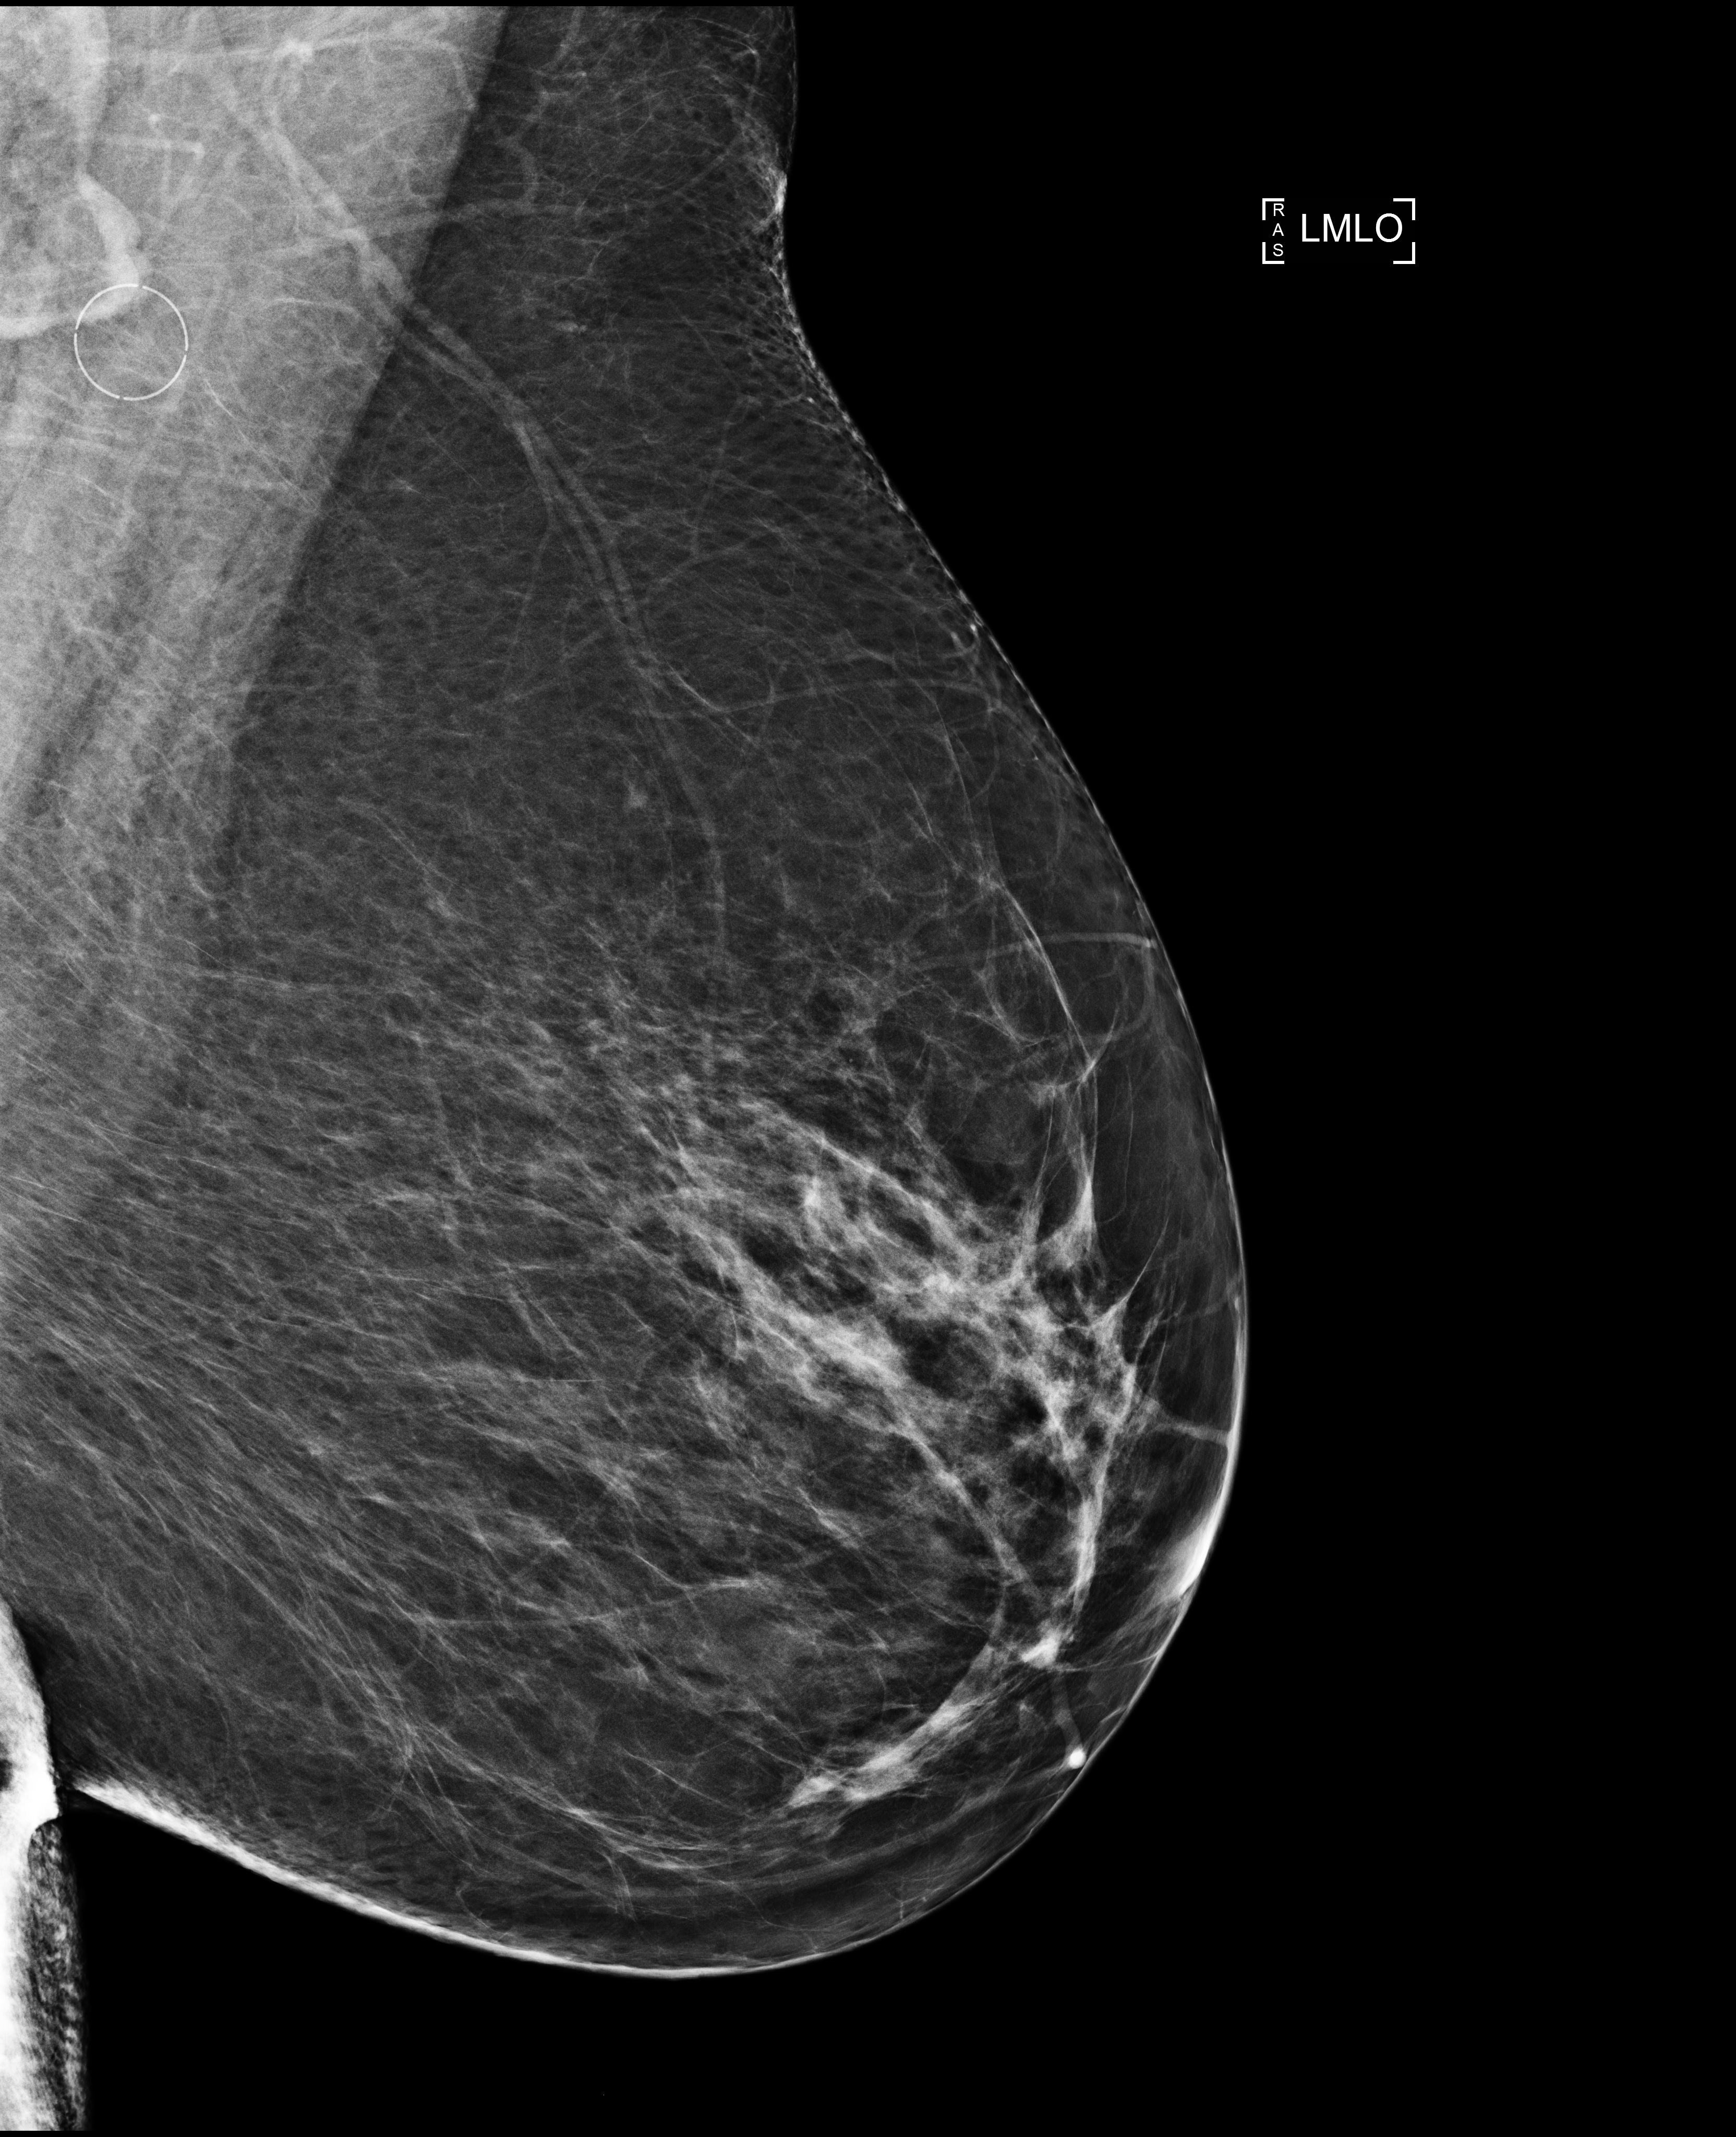
Full-field digital mammogram (FFDM), left breast, medio-lateral oblique projection, screening examination. Female patient, age 66 years.
Final BI-RADS category for the screening round (tomosynthesis exam, both breasts): category 1.